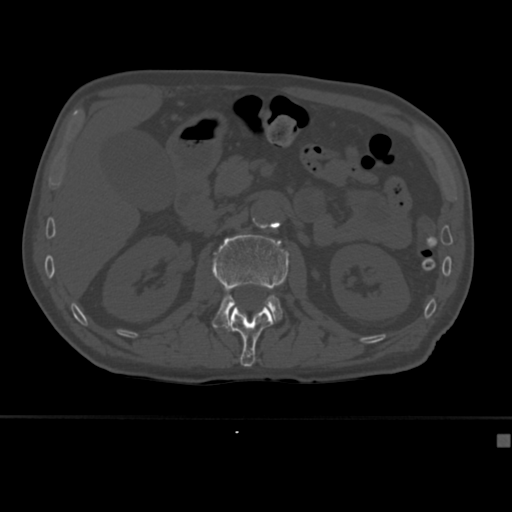
CT including the spine, one axial slice; position 159 of 430 along the scan axis; reconstruction kernel Br40s; bone window (W 1800 / L 400 HU); 512 × 512 image matrix, field of view 337 × 337 mm. Patient: male, 64 years. From the clinical record (not read from this slice): primary cancer: uterus; vertebrae with lytic lesions (as recorded): T1, T4, T5, T7, L5.
Structures marked on this image (semi-automatic segmentation, software-assisted and operator-edited):
- L1 vertebra: box from (x=229, y=307) to (x=274, y=367) px
- L2 vertebra: (x=212, y=233)–(x=289, y=332)